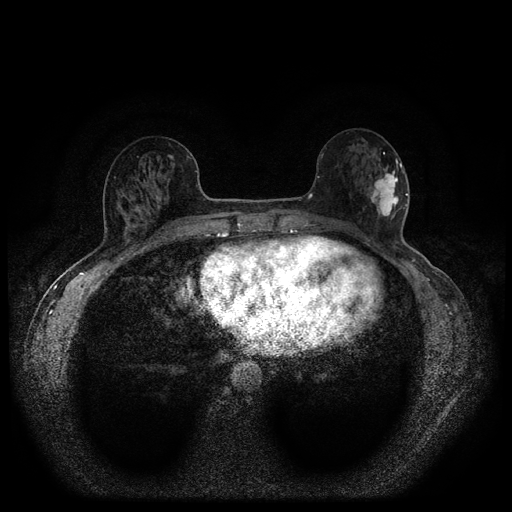
Breast MRI (dynamic contrast-enhanced, multi-phase), one axial slice; slice 43 of 116 in the series (ordered by position); dynamic contrast-enhanced series, time point 2 of 5 at this slice position (early post-contrast); 1.5 T; TE 2.7 ms, TR 5.4 ms; 512 × 512 image matrix, field of view 330 × 330 mm. Patient: female, 56 years.
Outlined on this slice (semi-automatic segmentation, software-assisted and operator-edited):
- breast lesion (labelled 'tumour' in the annotation; benign lesions carry a separate 'benign' label): bounding box <369,164,402,220> (left, top, right, bottom; pixels)